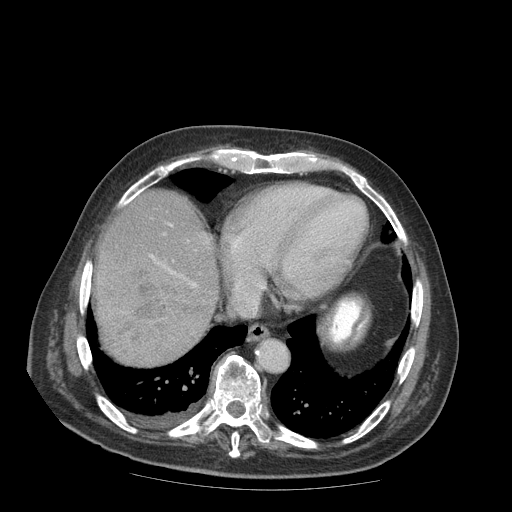
Contrast-enhanced abdominal CT (liver protocol), one axial slice; slice 80 of 99 in the series (ordered by position); reconstruction kernel STANDARD; 140 kVp; soft-tissue window (W 400 / L 40 HU); 2.5 mm slice thickness; 512 × 512 image matrix, field of view 420 × 420 mm. From the clinical record (not read from this slice): diagnosis: hepatocellular carcinoma (patient treated with transarterial chemoembolisation; whether this scan precedes or follows treatment is not stated here); TNM stage (as recorded): Stage-IIIB; Child-Pugh class: A; tumour differentiation: well differentiated.
Annotated regions visible in this slice (semi-automatically segmented with operator editing):
- liver parenchyma outside the tumour (the mass and vessels are separate outlines, so this box may not span the whole liver): bounding box <94,190,218,309> (left, top, right, bottom; pixels)
- mass: <95,252,214,368>
- liver vessels: <150,223,197,288>